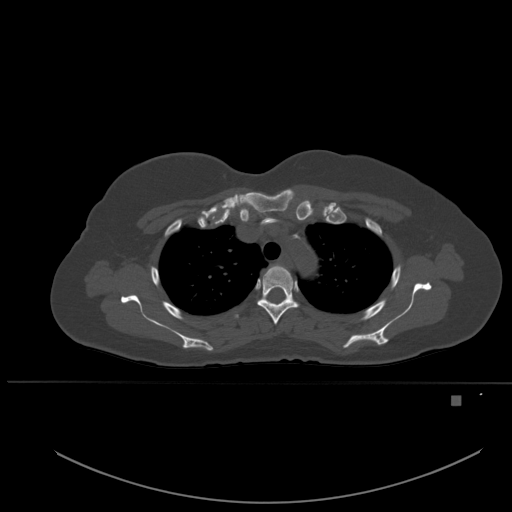
CT including the spine, one axial slice. Position 393 of 651 along the scan axis. Bone window (W 1800 / L 400 HU). 1.5 mm slice thickness. 512 × 512 image matrix, field of view 443 × 443 mm. Female patient, age 49 years. From the clinical record (not read from this slice): primary cancer: breast; vertebrae with lytic lesions (as recorded): L3, T12, L4.
Outlined on this slice (semi-automatically segmented with operator editing):
- T3 vertebra: bounding box <257,265,299,325> (left, top, right, bottom; pixels)